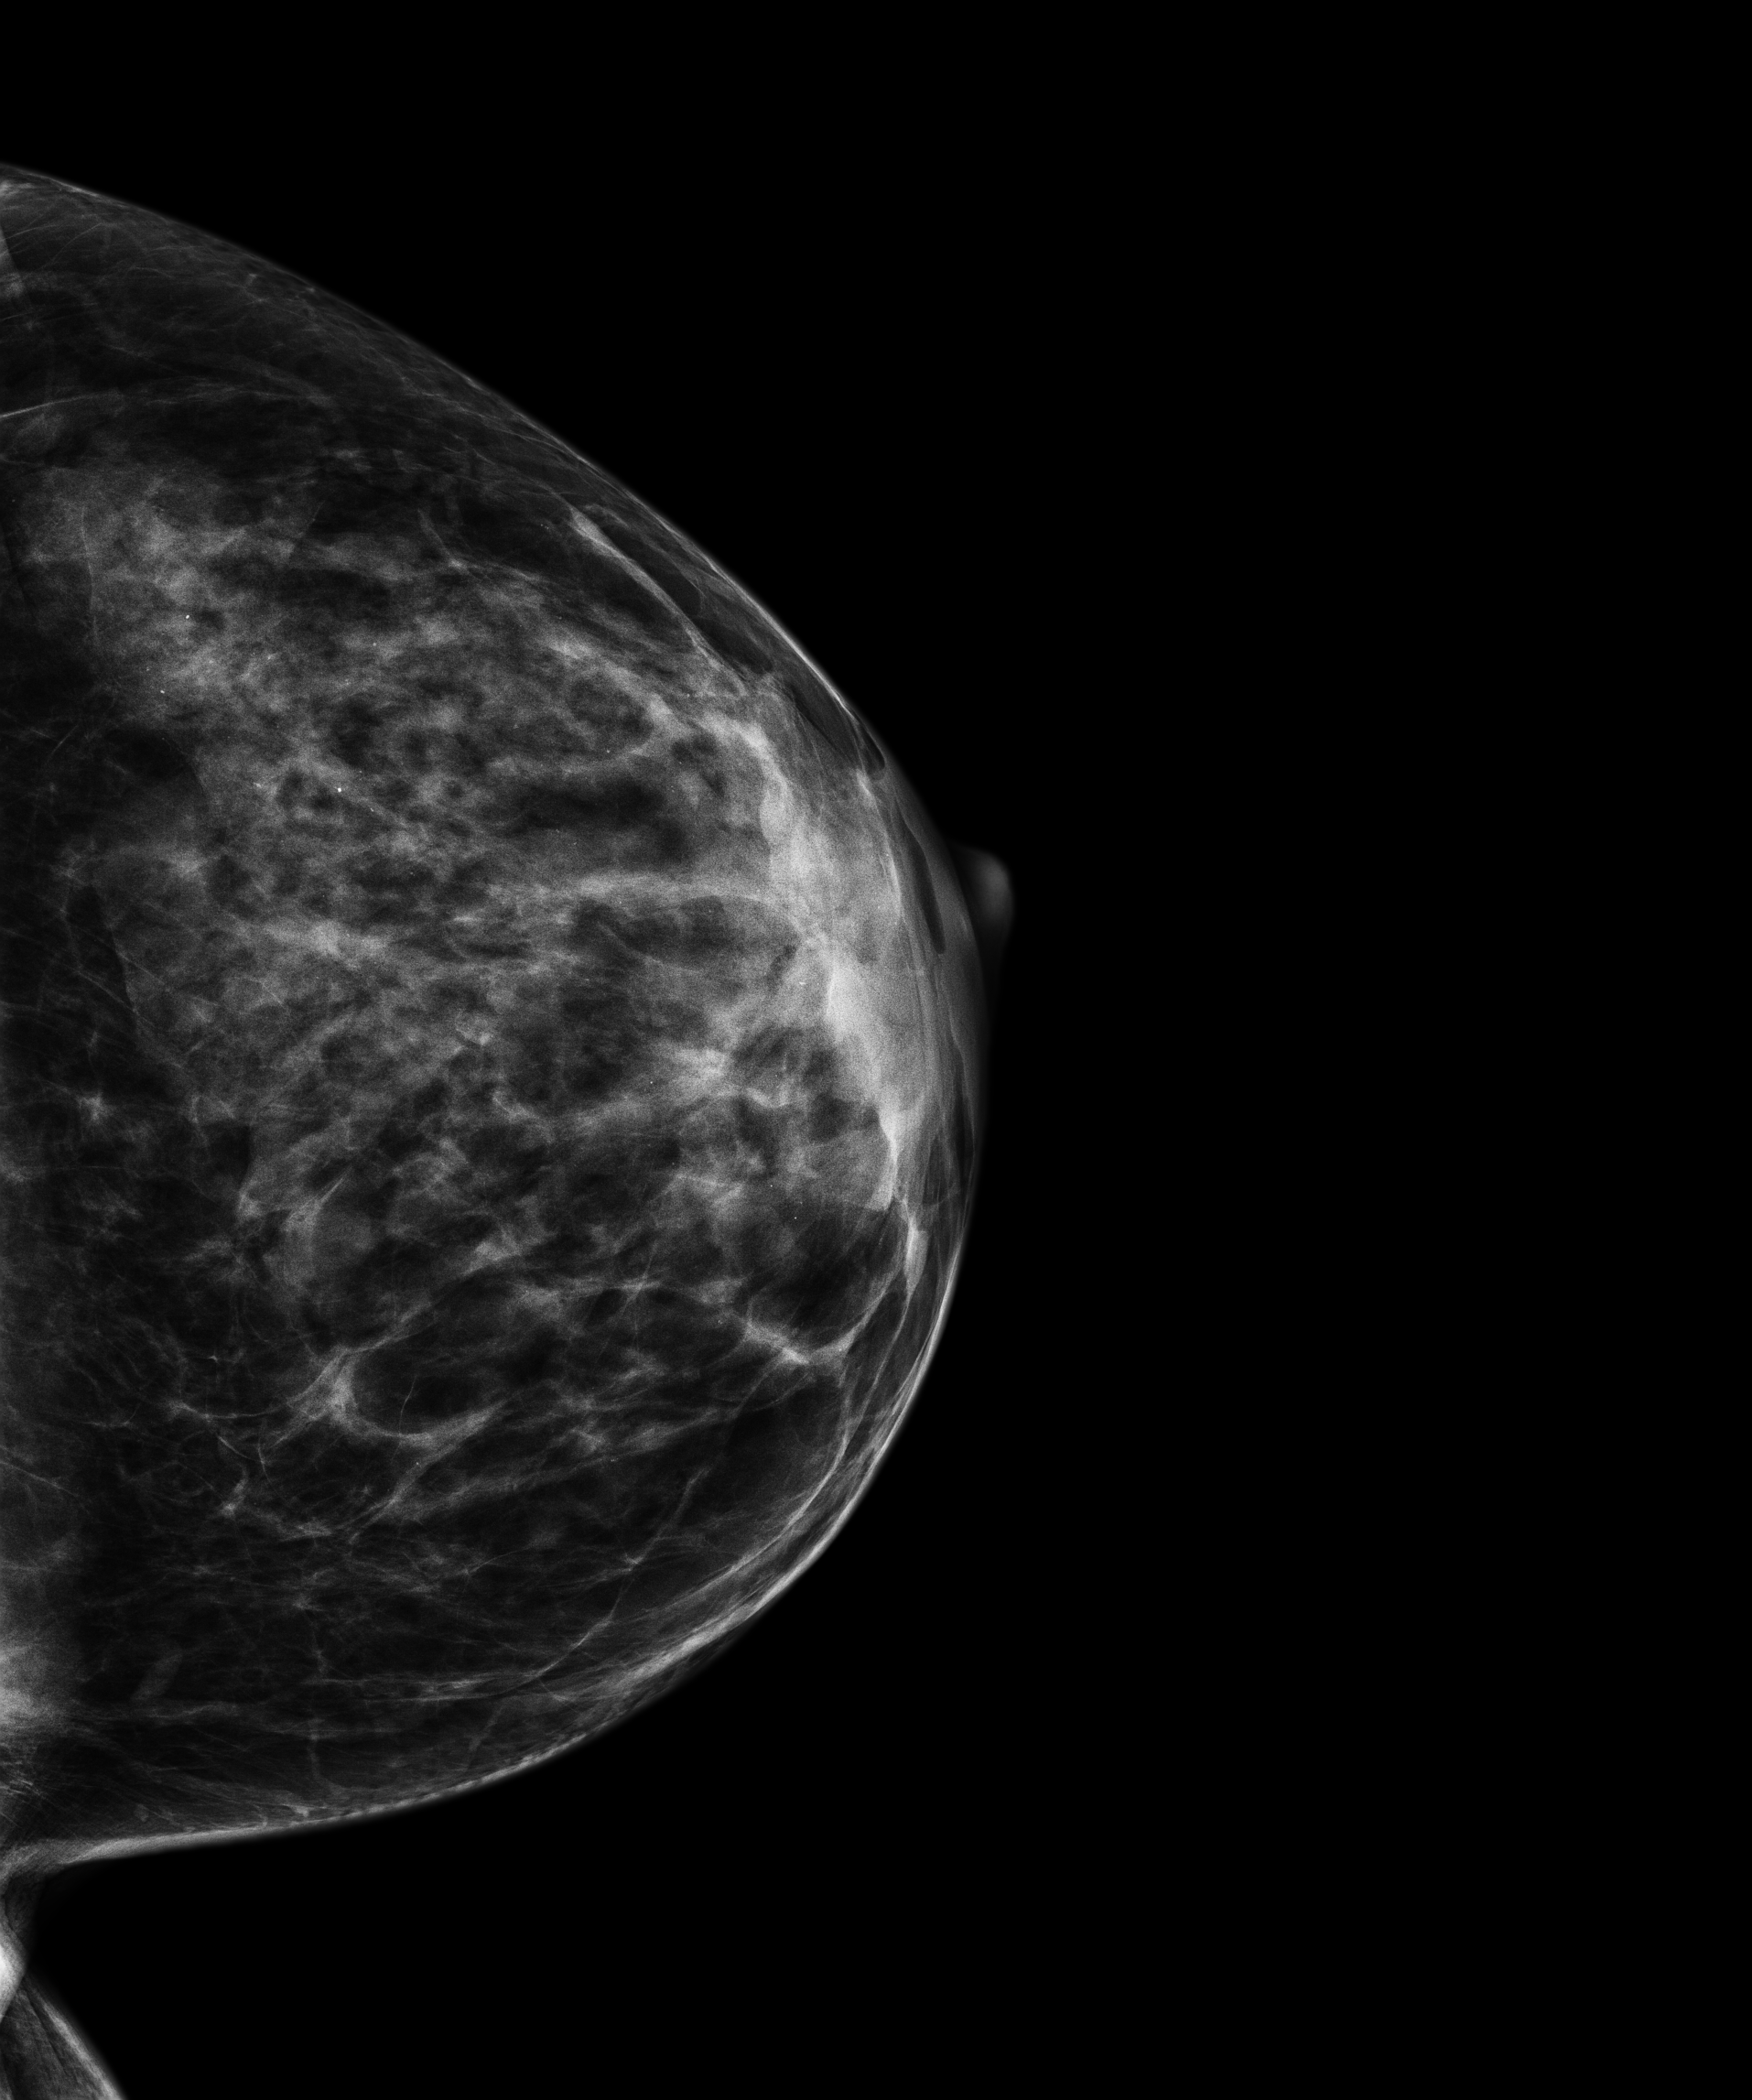
Screening examination, system: Senographe Pristina. Female patient, age 48 years.
Image type: full-field digital mammogram. Breast: left. Projection: craniocaudal (CC) view.